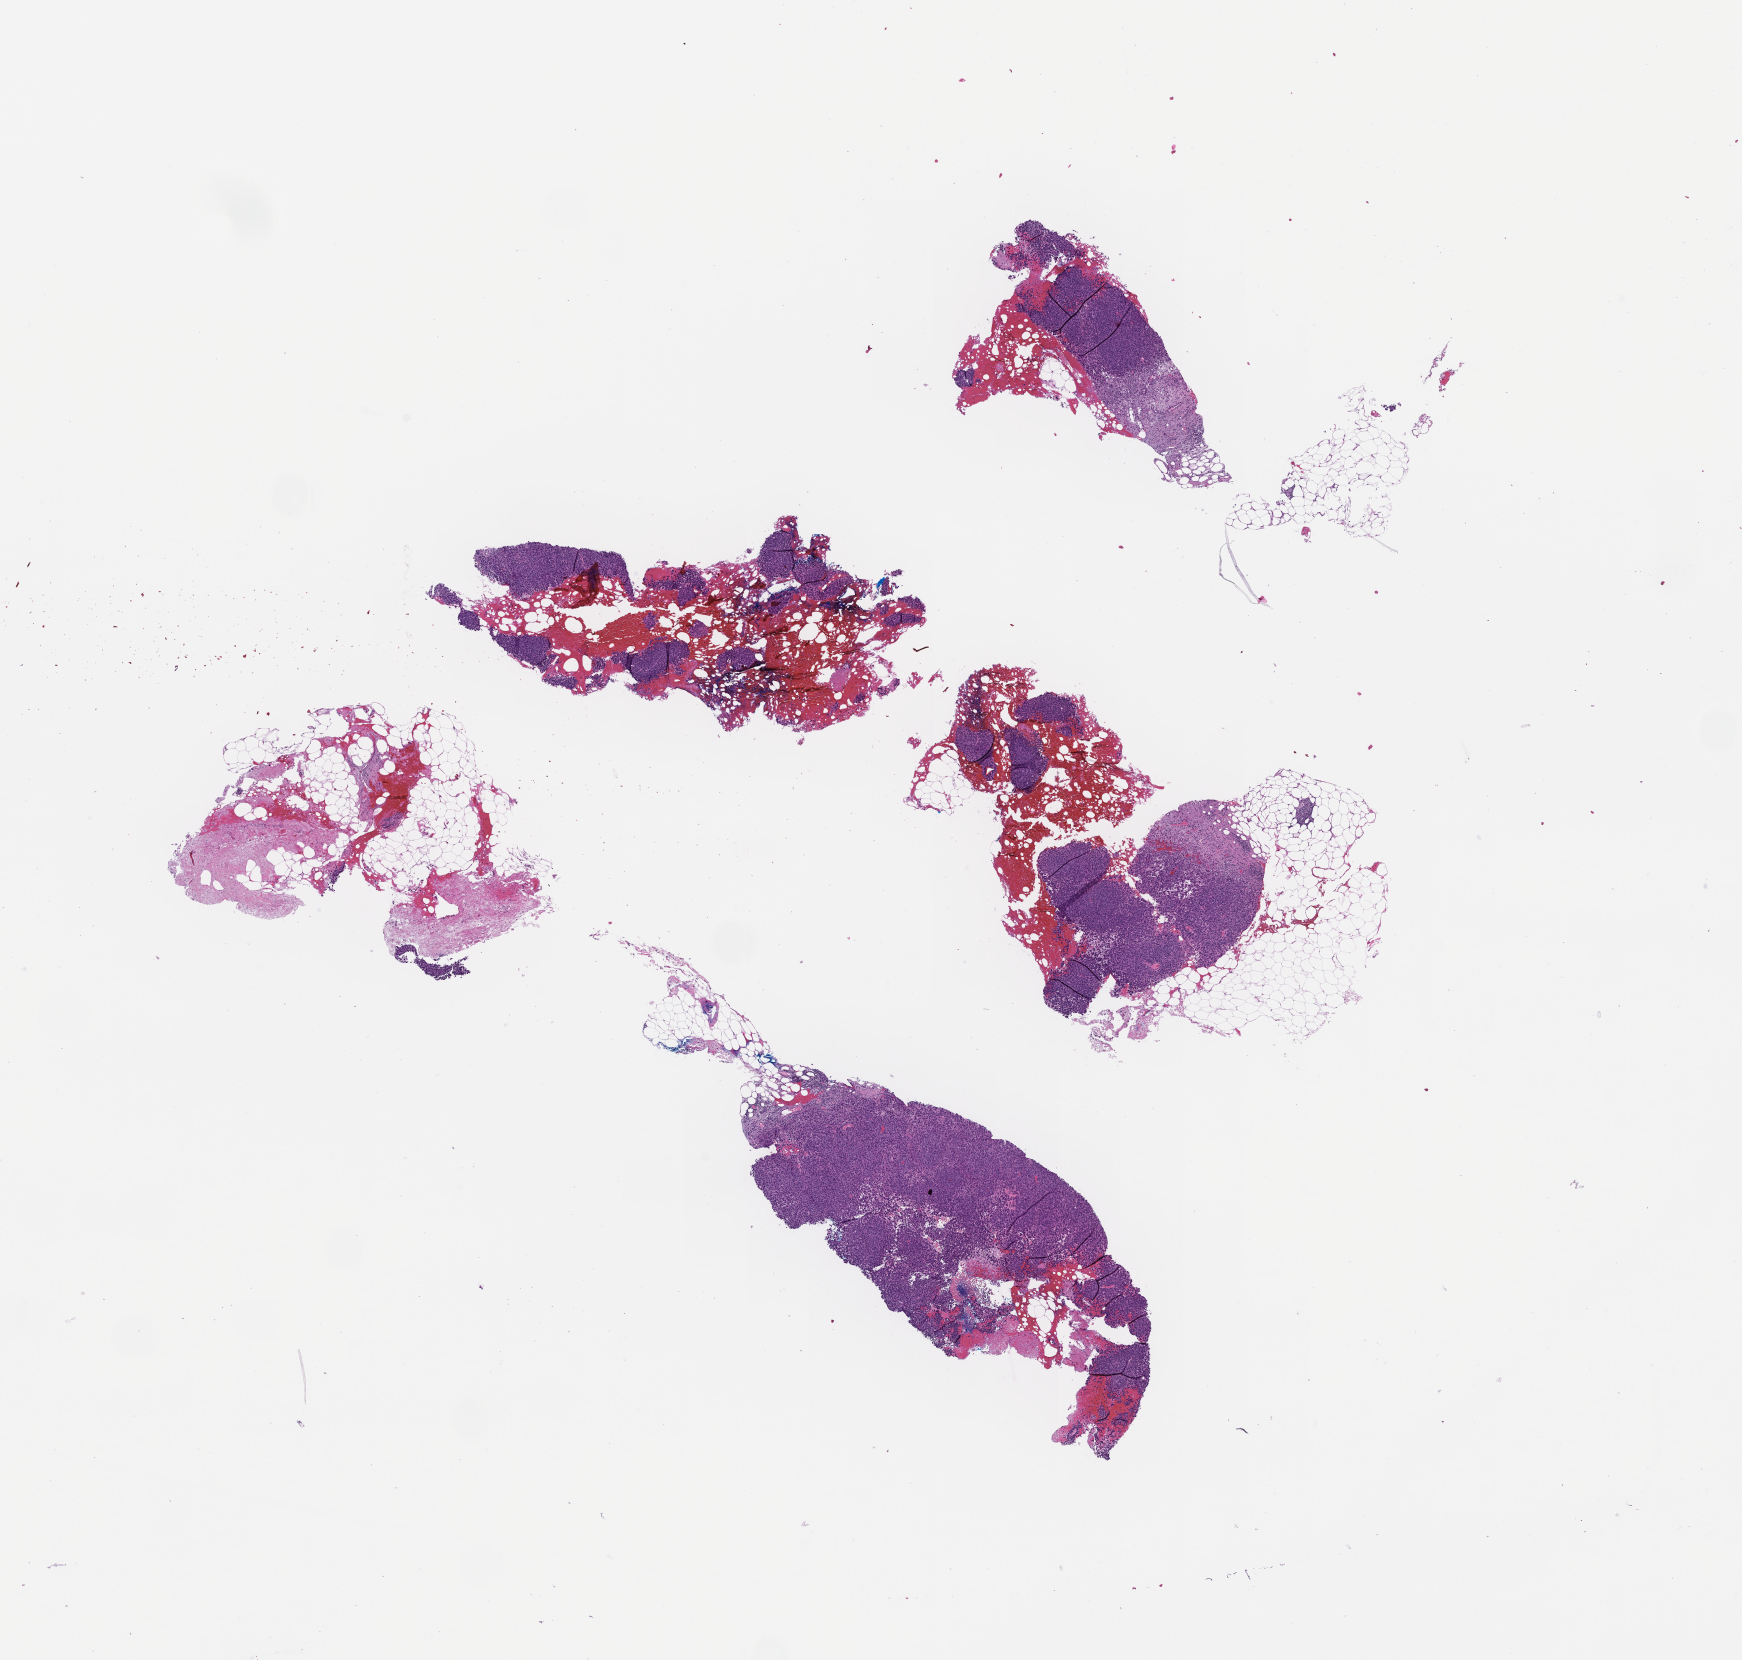
Digitized haematoxylin and eosin-stained section — whole scanned area (about 14.1 x 13.4 mm) shown as a low-resolution overview, FFPE section. Patient sex: female.
This section: metastasis (sampled organ not recorded). Patient diagnosis (primary): Melanoma.